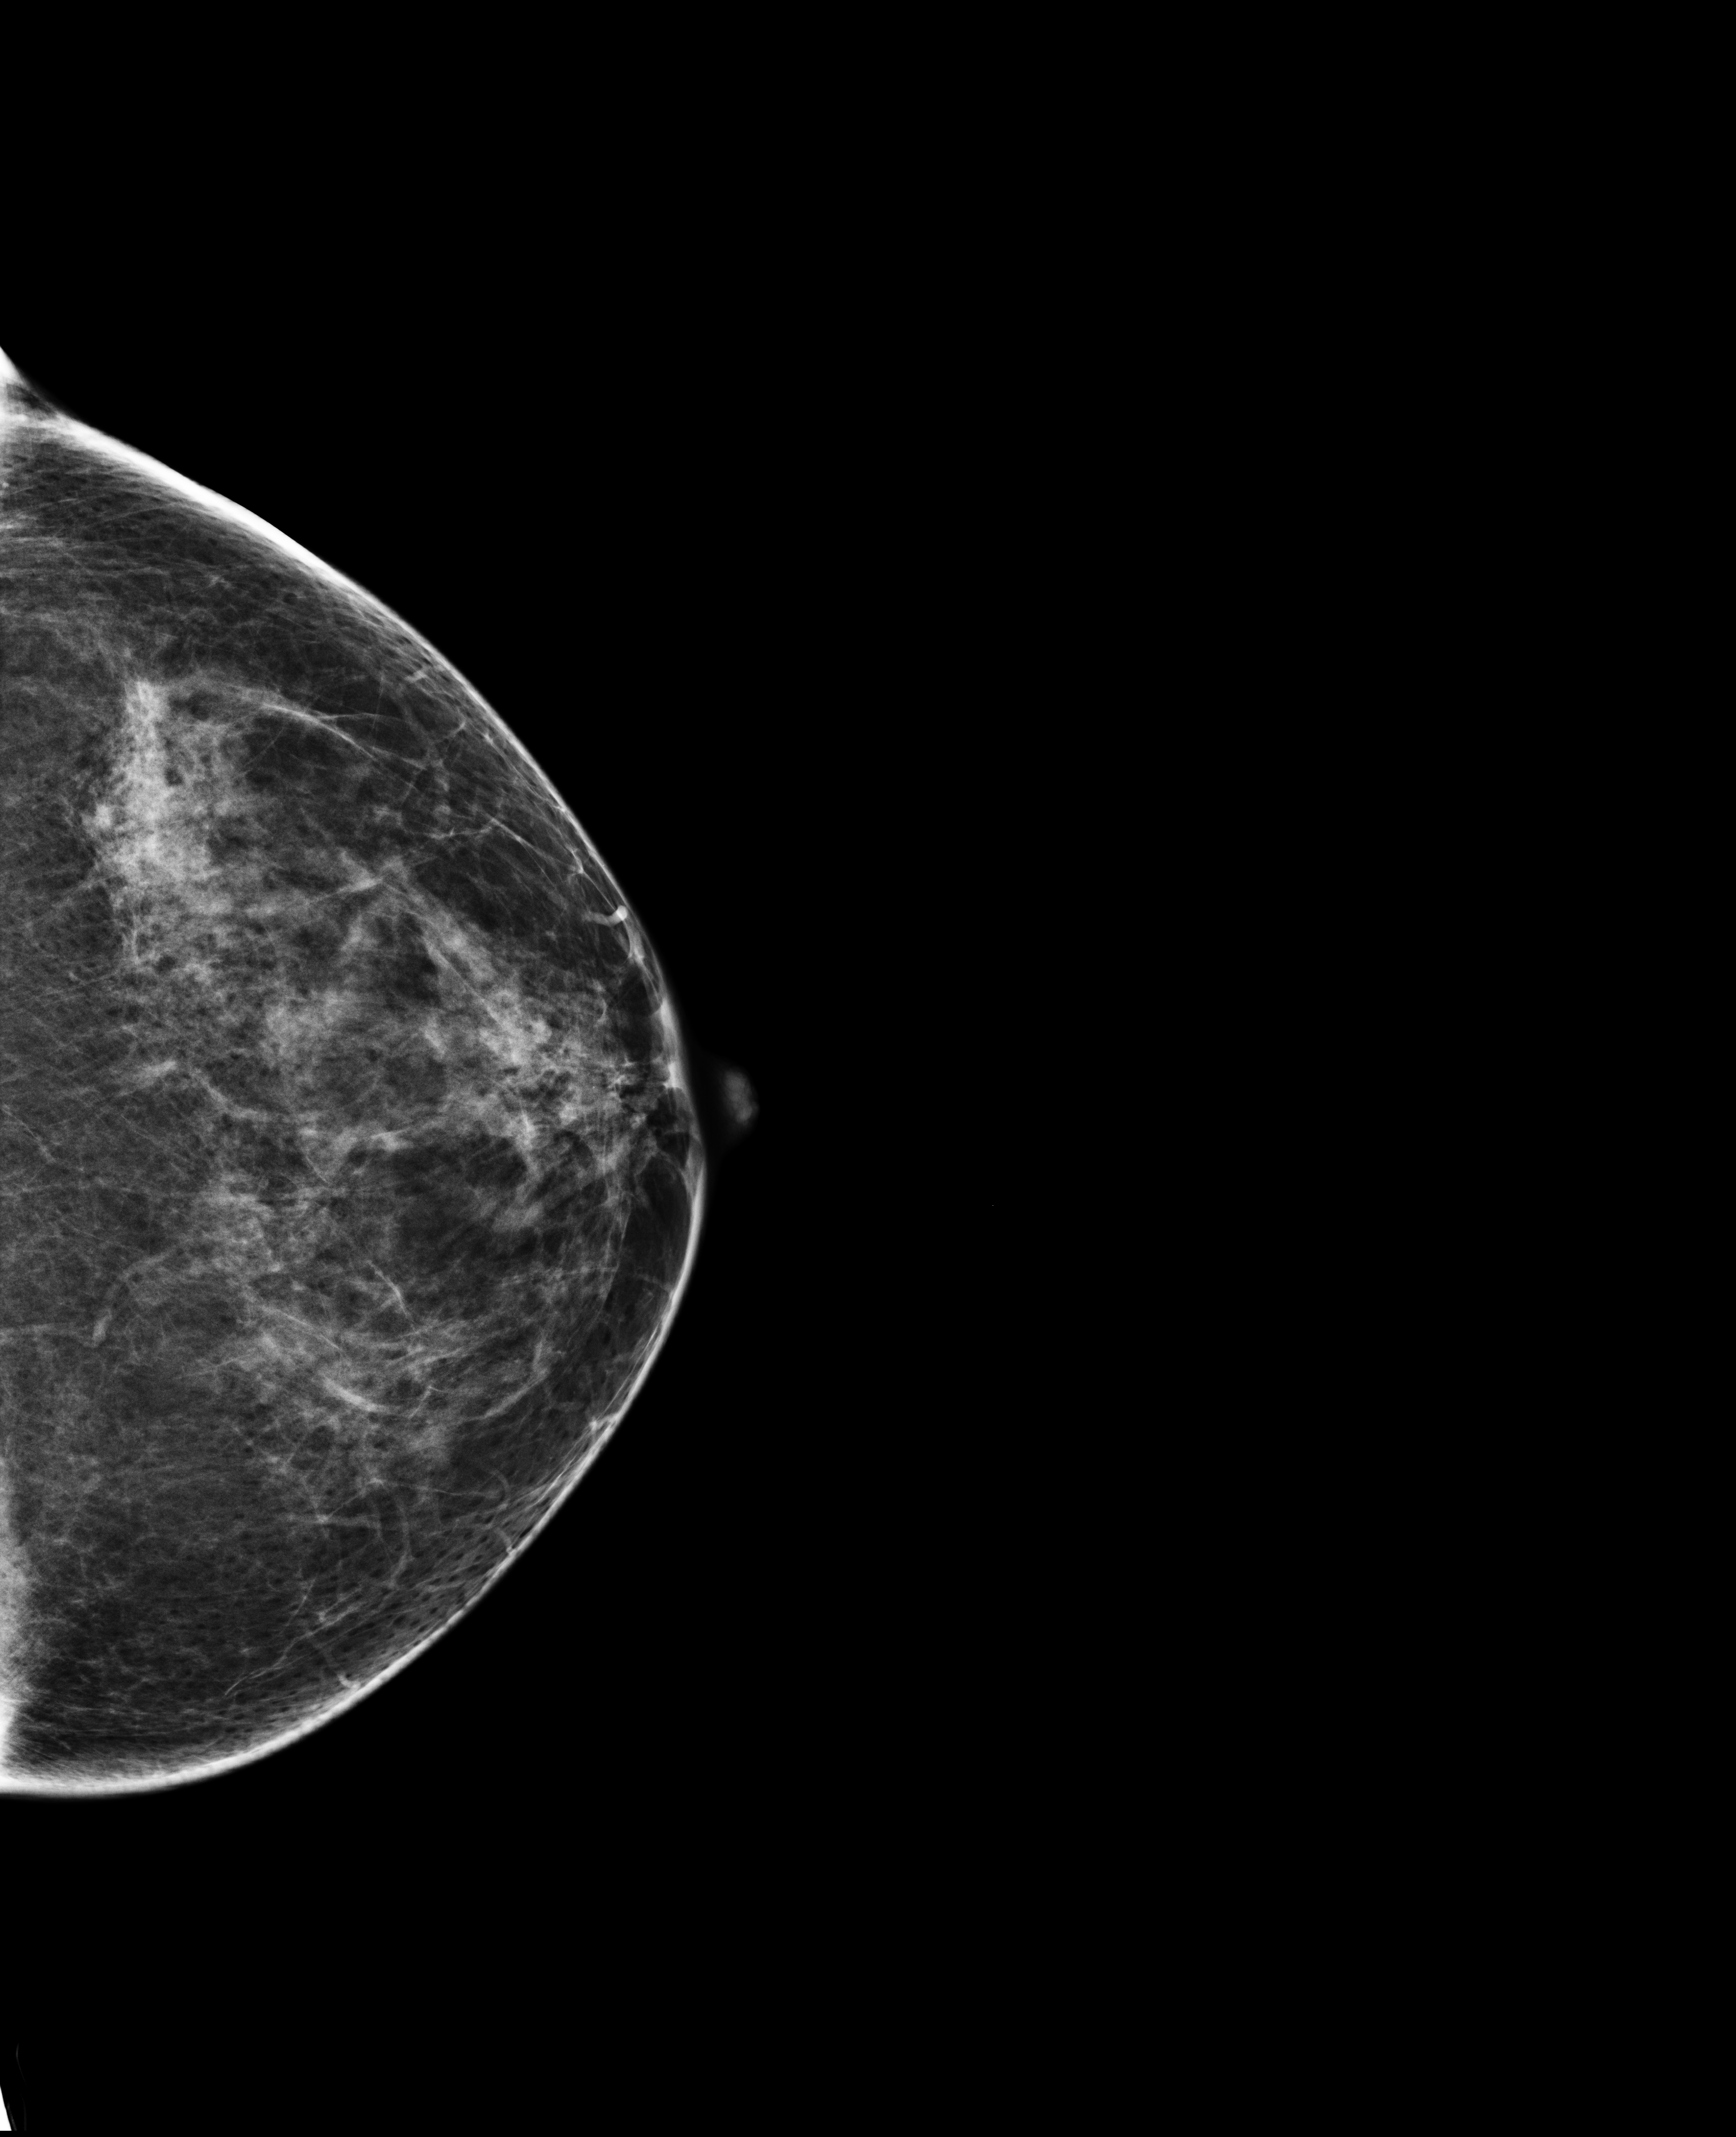
Screening examination, system: Selenia Dimensions. Female patient, age 52 years.
Image type: full-field digital mammogram. Breast: left. Projection: craniocaudal (CC) view.